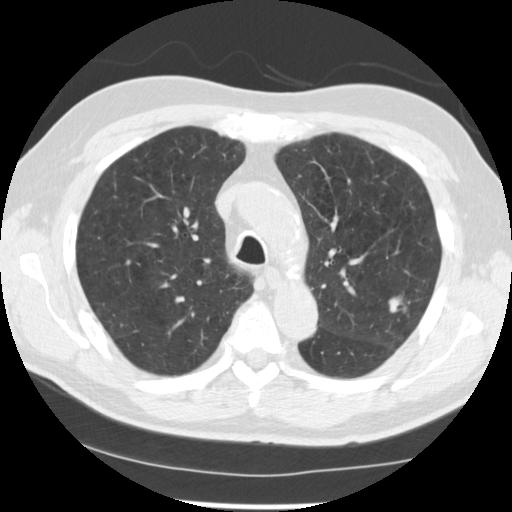
Low-dose screening chest CT, one axial slice; slice 176 of 249 in the series (ordered by position); reconstruction kernel STANDARD; 120 kVp; lung window (W 1500 / L -600 HU); 2.5 mm slice thickness; 512 × 512 image matrix, field of view 341 × 341 mm.
Structures marked on this image (outlined manually by an expert reader):
- lesion 1 (tumor, upper lobe of left lung): bounding box <389,297,402,312> (left, top, right, bottom; pixels)